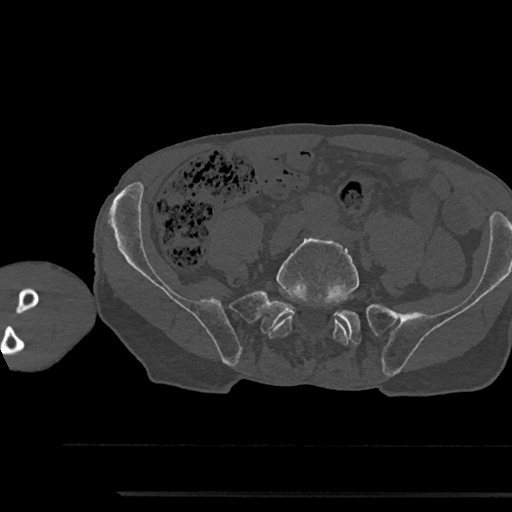
CT including the spine, one axial slice. Position 326 of 797 along the scan axis. Reconstruction kernel Br40s/3. Bone window (W 1800 / L 400 HU). 512 × 512 image matrix, field of view 367 × 367 mm. Male patient, age 79 years. From the clinical record (not read from this slice): primary cancer: prostate.
Annotated regions visible in this slice (semi-automatically segmented with operator editing):
- L5 vertebra: bounding box <267,238,359,344> (left, top, right, bottom; pixels)